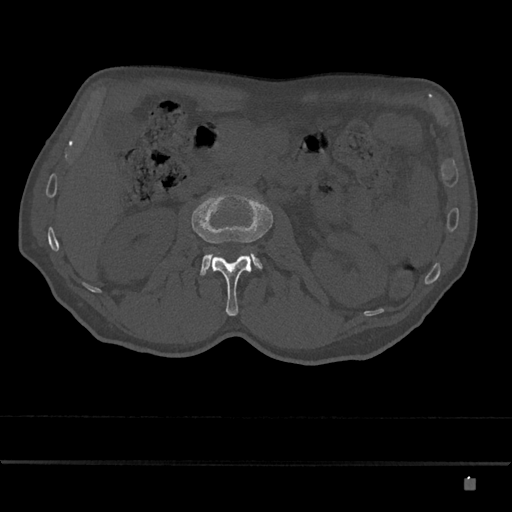
CT including the spine, one axial slice. Position 458 of 797 along the scan axis. Reconstruction kernel Br40s/3. Bone window (W 1800 / L 400 HU). 512 × 512 image matrix, field of view 390 × 390 mm. Patient: male, 72 years. Case-level facts recorded for this patient, not image findings: primary cancer: prostate.
Structures marked on this image (semi-automatic segmentation, software-assisted and operator-edited):
- L2 vertebra: bounding box (x1, y1, x2, y2) in pixels: (192, 194, 273, 316)
- L3 vertebra: (200, 253, 263, 276)